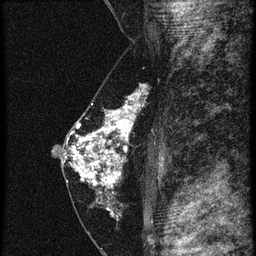
Breast MRI (dynamic contrast-enhanced), one sagittal slice; position 31 of 60 along the scan axis; 4 images stored at this slice position (order not interpretable as contrast timing); 1.5 T; TE 4.2 ms, TR 20.4 ms; 1.5 mm slice thickness; 256 × 256 image matrix, field of view 180 × 180 mm. Female patient, age 46 years. From the clinical record (not read from this slice): setting: breast cancer imaged before/during neoadjuvant chemotherapy; receptor status: triple-negative.
Structures marked on this image (semi-automatic segmentation, software-assisted and operator-edited):
- analysis volume of interest (the breast-tissue region the enhancement analysis was run in; not a lesion): box from (x=67, y=86) to (x=152, y=201) px
- tumour enhancement mask (voxels above the 90 % enhancement threshold inside the analysis volume of interest): (x=69, y=94)–(x=142, y=195)